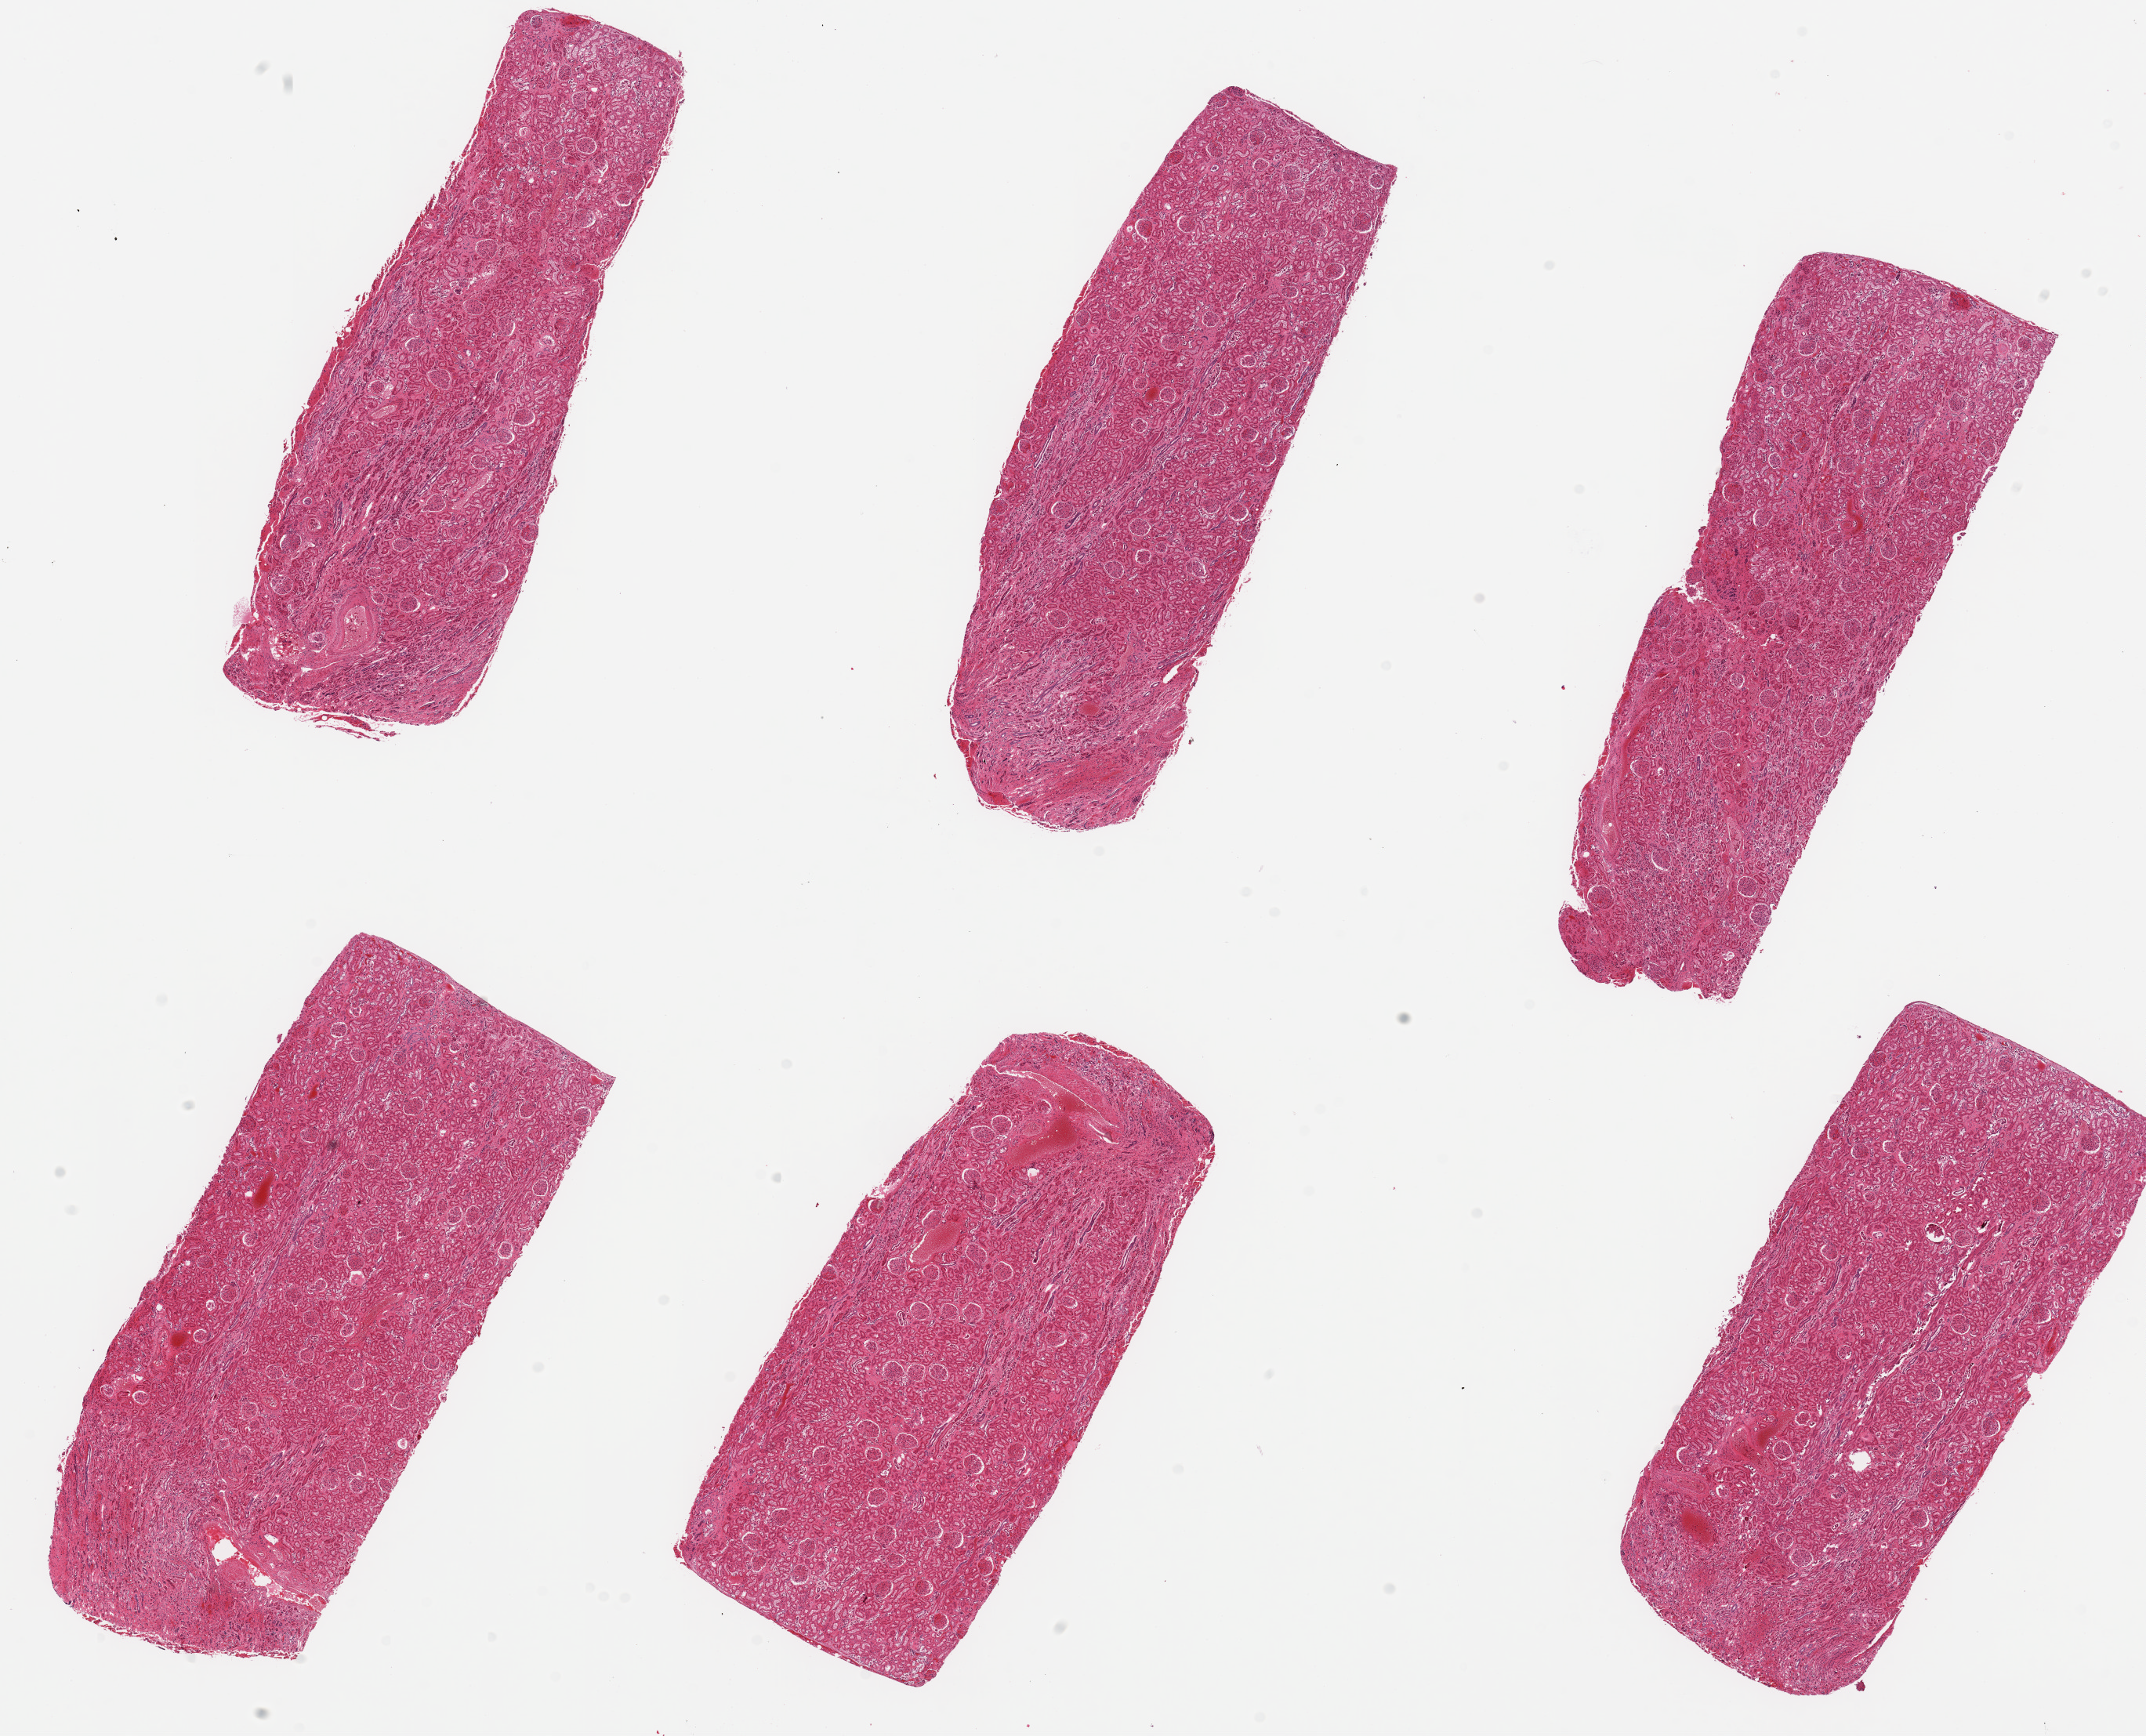
H&E whole-slide image — a low-resolution overview of the entire scanned area, about 21.7 x 17.5 mm (slide scanned at 20x). PAXgene-fixed paraffin-embedded (PFPE) section. Sampled site (target tissue): renal cortex. Tissue donor sample.
- reviewer comment on this tissue sample: 6 pieces, up to 8x3mm